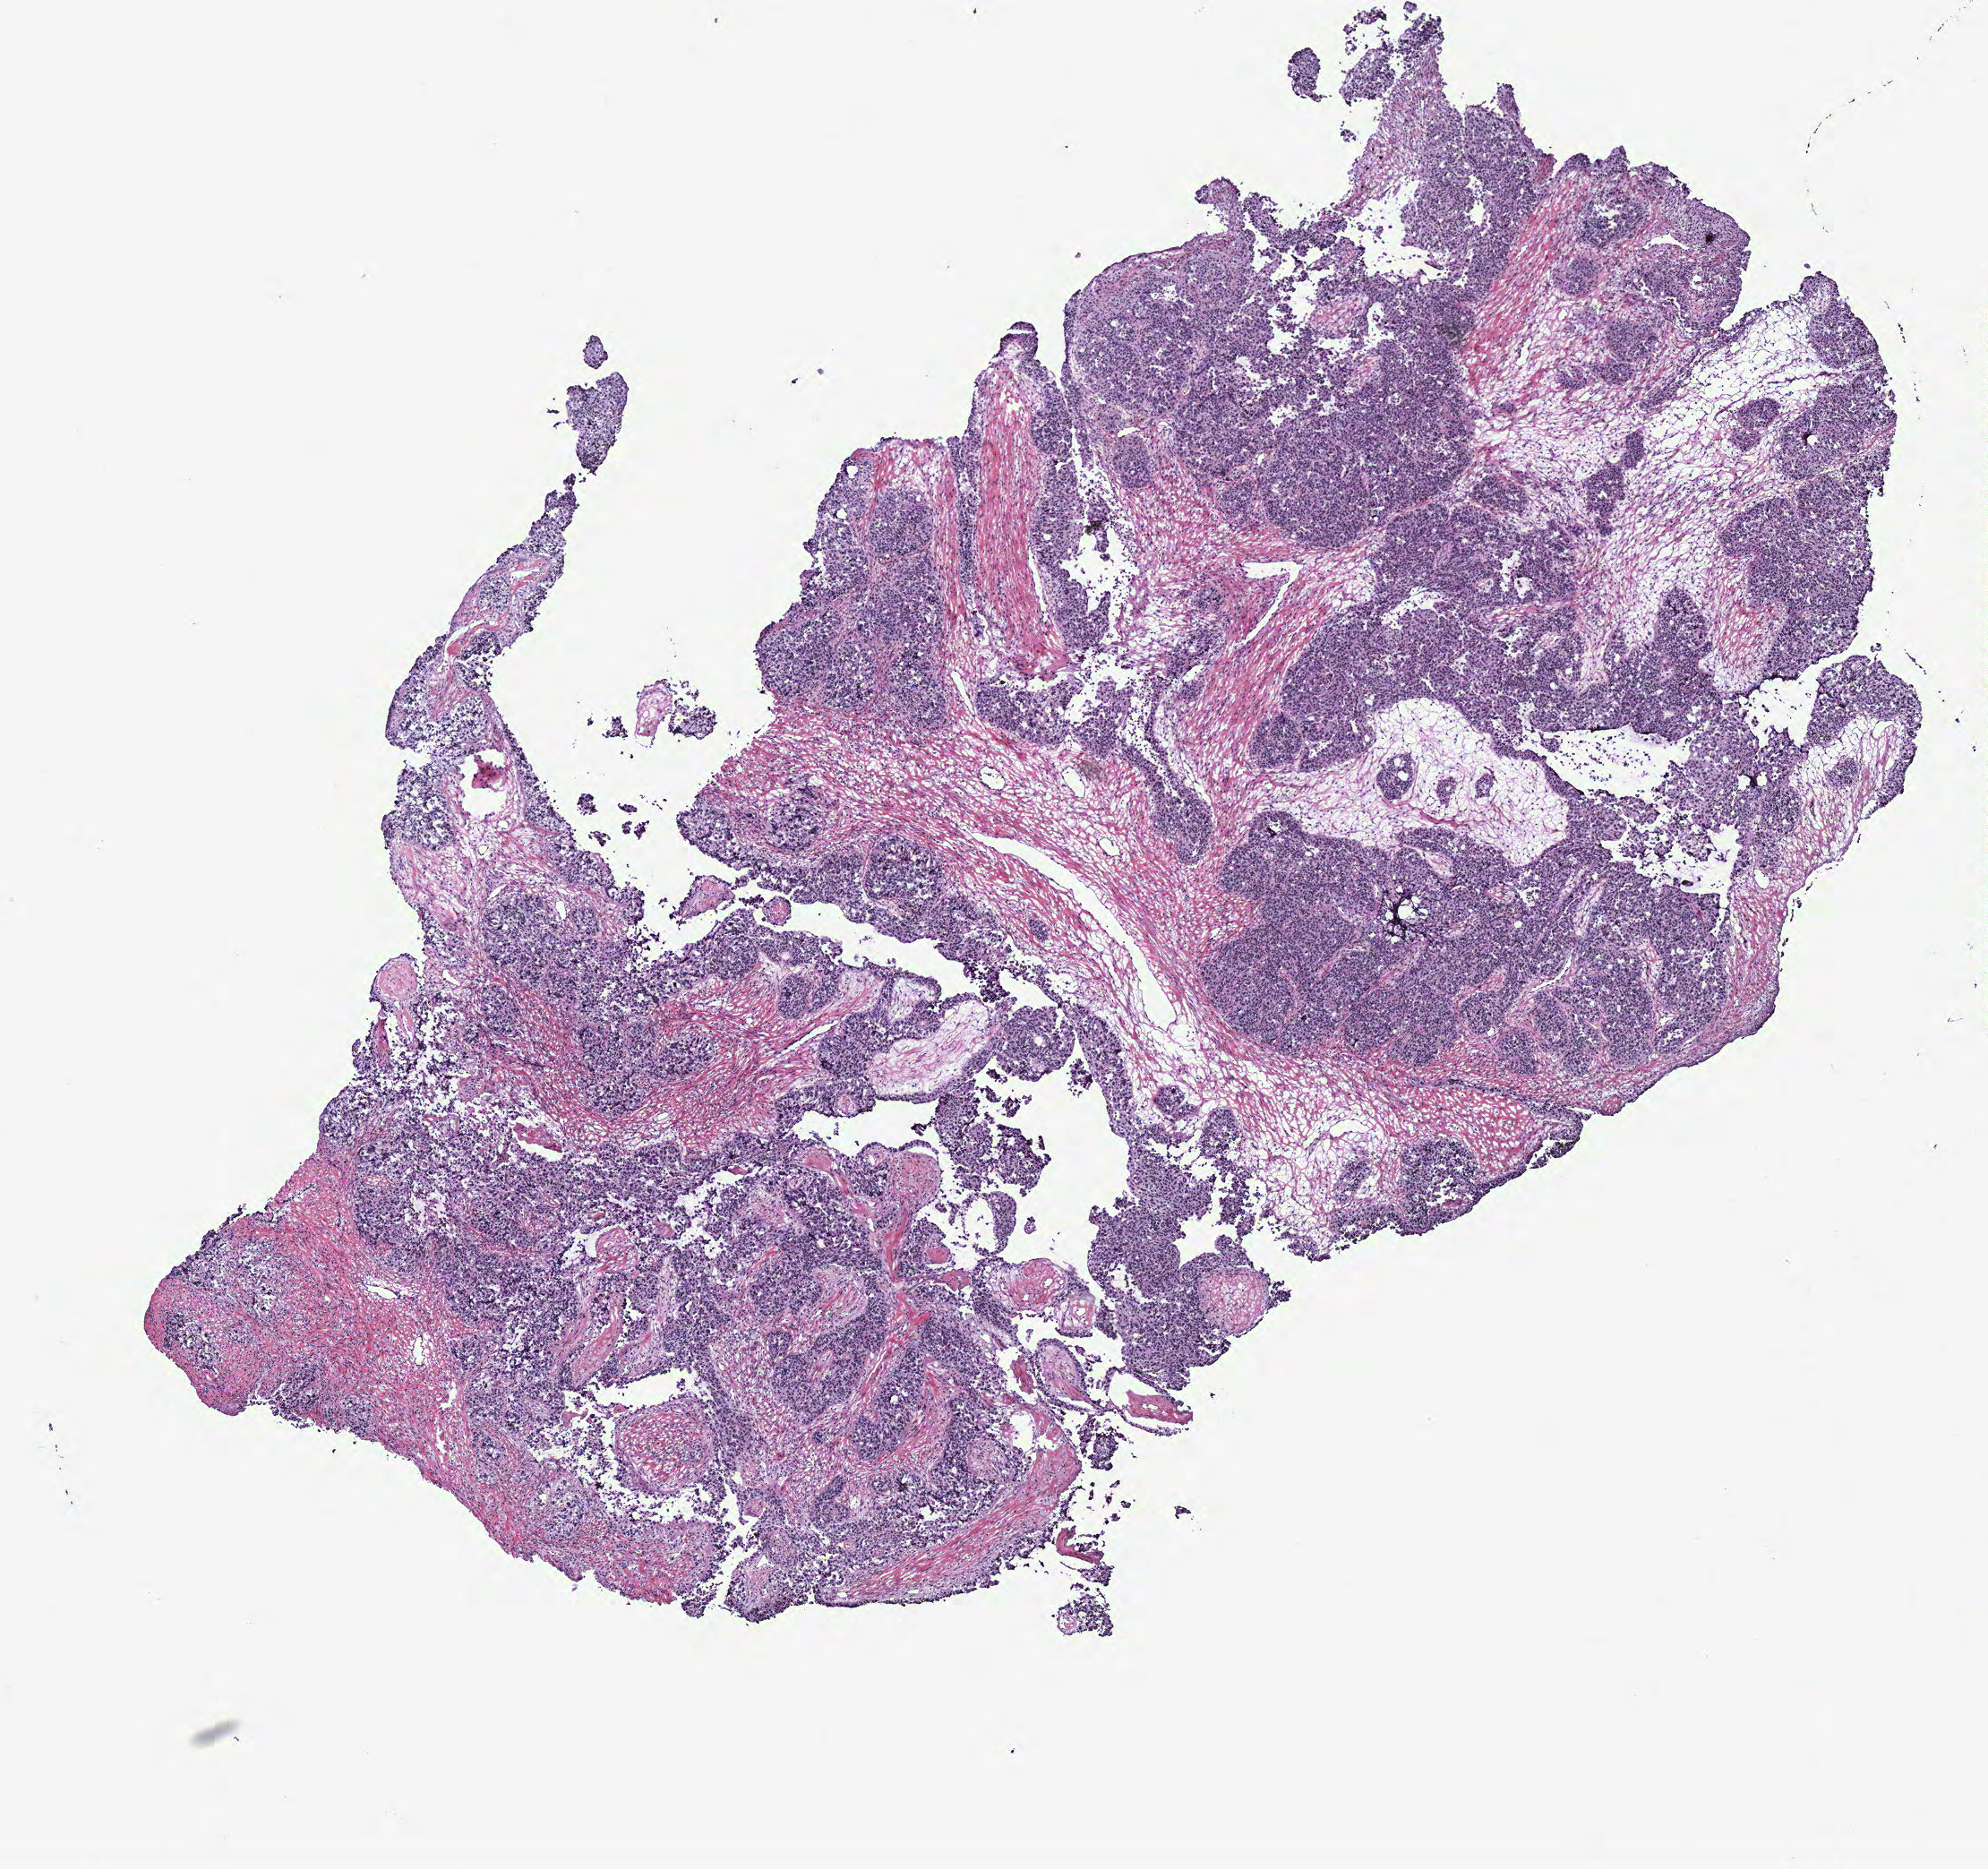
Hematoxylin and eosin (H&E) stained whole-slide image — shown as a low-resolution overview of the whole scanned area (about 8.9 x 8.4 mm, from a 40x scan), ovary, tissue type not recorded.
Patient diagnosis (cohort enrolment): ovarian cancer (ovary).